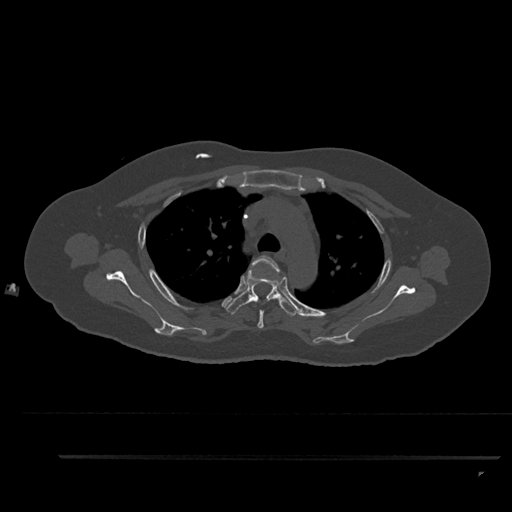
CT including the spine, one axial slice. Position 658 of 797 along the scan axis. Reconstruction kernel Br40s/3. Bone window (W 1800 / L 400 HU). 512 × 512 image matrix, field of view 408 × 408 mm. Female patient, age 44 years. From the clinical record (not read from this slice): primary cancer: renal; vertebrae with lytic lesions (as recorded): L1.
Annotated regions visible in this slice (semi-automatically segmented with operator editing):
- T3 vertebra: bounding box (x1, y1, x2, y2) in pixels: (250, 255, 282, 329)
- T4 vertebra: (226, 268, 299, 316)